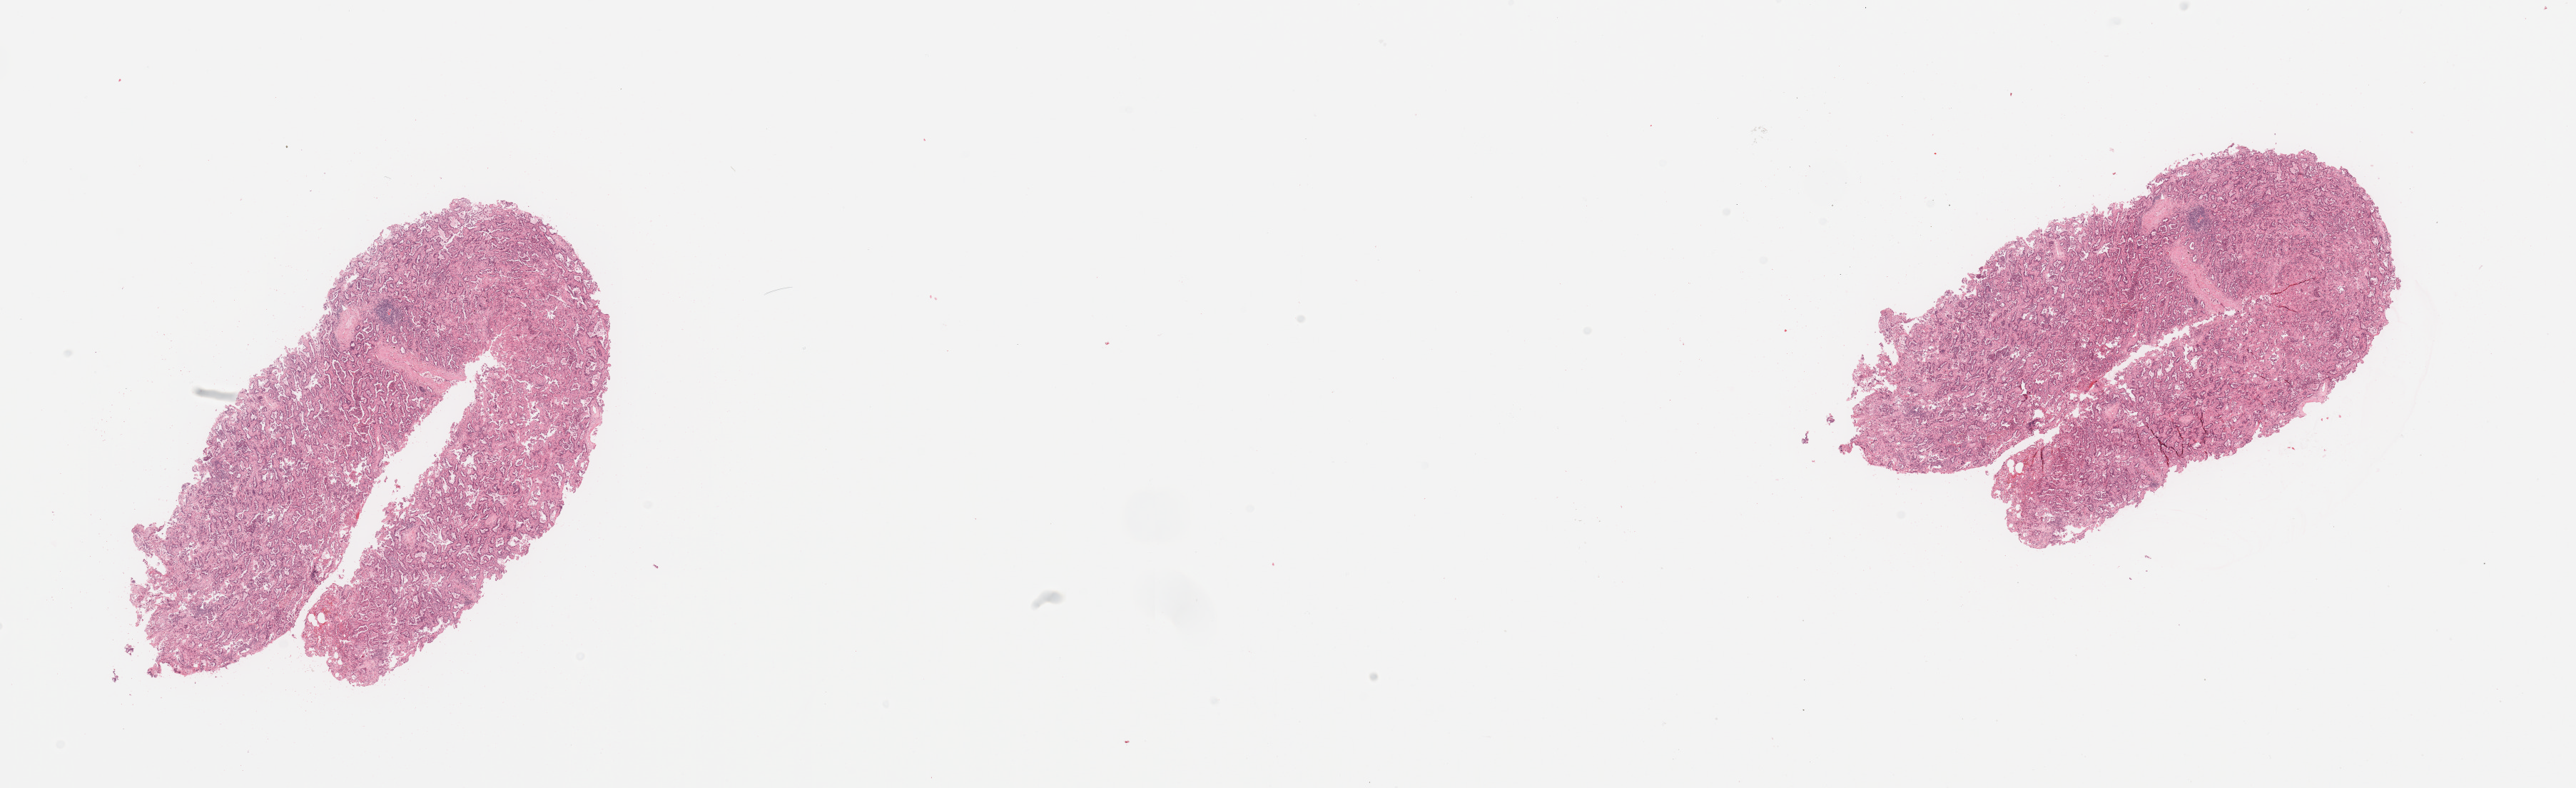
H&E whole-slide image, a low-resolution overview of the entire scanned area, about 28.5 x 8.7 mm (acquisition: 20x scan); tumour tissue sample, sampled site: lung. 72-year-old female patient.
Histologic diagnosis: Adenocarcinoma, NOS.